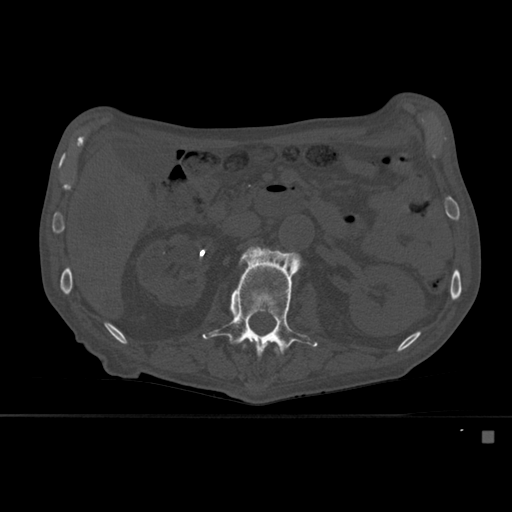
CT including the spine, one axial slice; slice 237 of 527 in the series (ordered by position); bone window (W 1800 / L 400 HU); 1.5 mm slice thickness; 512 × 512 image matrix, field of view 373 × 373 mm. Patient: male, 78 years. From the clinical record (not read from this slice): primary cancer: prostate.
Annotated regions visible in this slice (semi-automatic segmentation, software-assisted and operator-edited):
- L1 vertebra: box from (x=243, y=344) to (x=282, y=356) px
- L2 vertebra: (x=202, y=246)–(x=318, y=360)